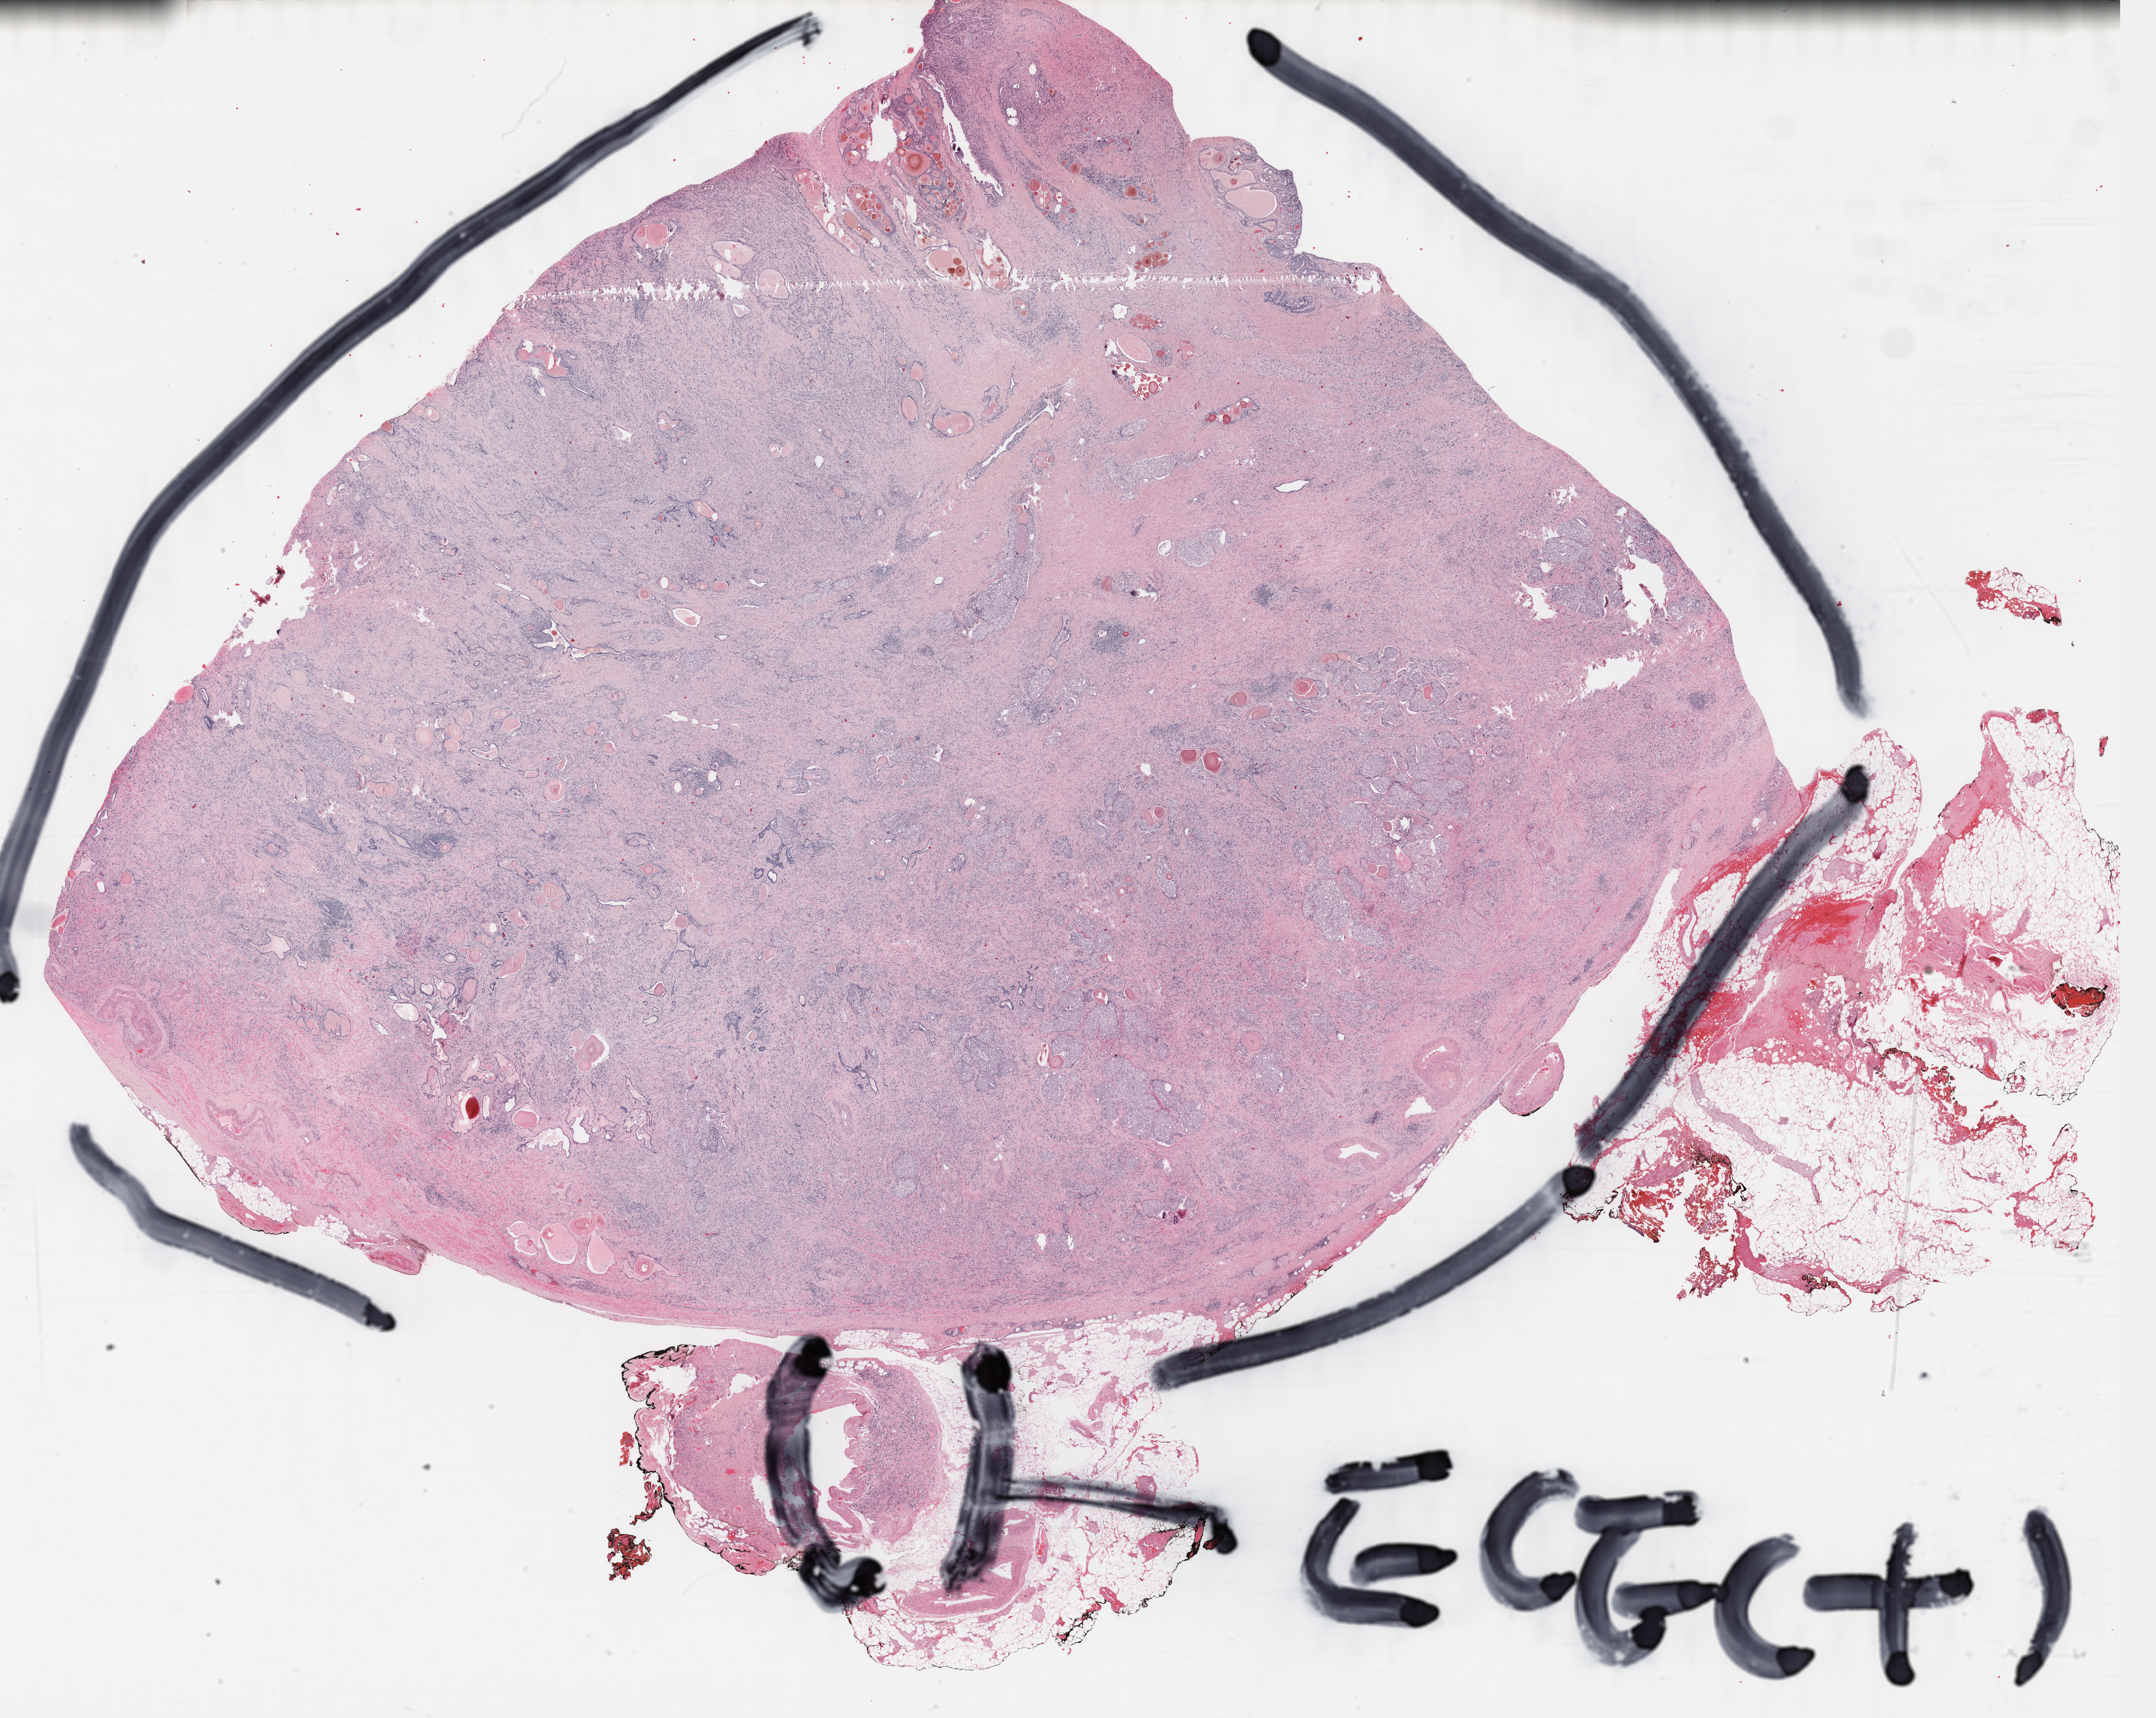
Whole-slide histology image, Hematoxylin and eosin (H&E) stained, shown as a low-resolution overview of the whole scanned area (about 28.7 x 22.9 mm, from a 40x scan); FFPE section; prostate, primary tumour sample. Male, age 57 years at initial diagnosis. Gleason score: 9 (5+4).
* lymph nodes positive (case pathology): 11 of 19 examined
* laterality: bilateral
* pathologic diagnosis: Adenocarcinoma, NOS (prostate gland)